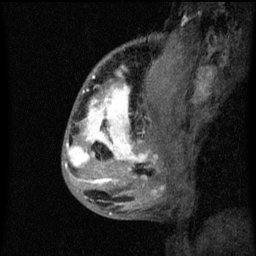
Breast MRI (dynamic contrast-enhanced), one sagittal slice. Position 21 of 60 along the scan axis. Dynamic contrast-enhanced series, image 2 of 3 at this slice position (ordered by acquisition). 1.5 T. TE 4.2 ms, TR 8 ms. 2 mm slice thickness. 256 × 256 image matrix, field of view 180 × 180 mm. Female patient, age 50 years.
Annotated regions visible in this slice (semi-automatically segmented with operator editing):
- analysis volume of interest (the breast-tissue region the enhancement analysis was run in; not a lesion): bounding box [x1, y1, x2, y2] px = [66, 64, 141, 187]
- tumour enhancement mask (voxels above the 70 % enhancement threshold inside the analysis volume of interest): [66, 84, 141, 185]